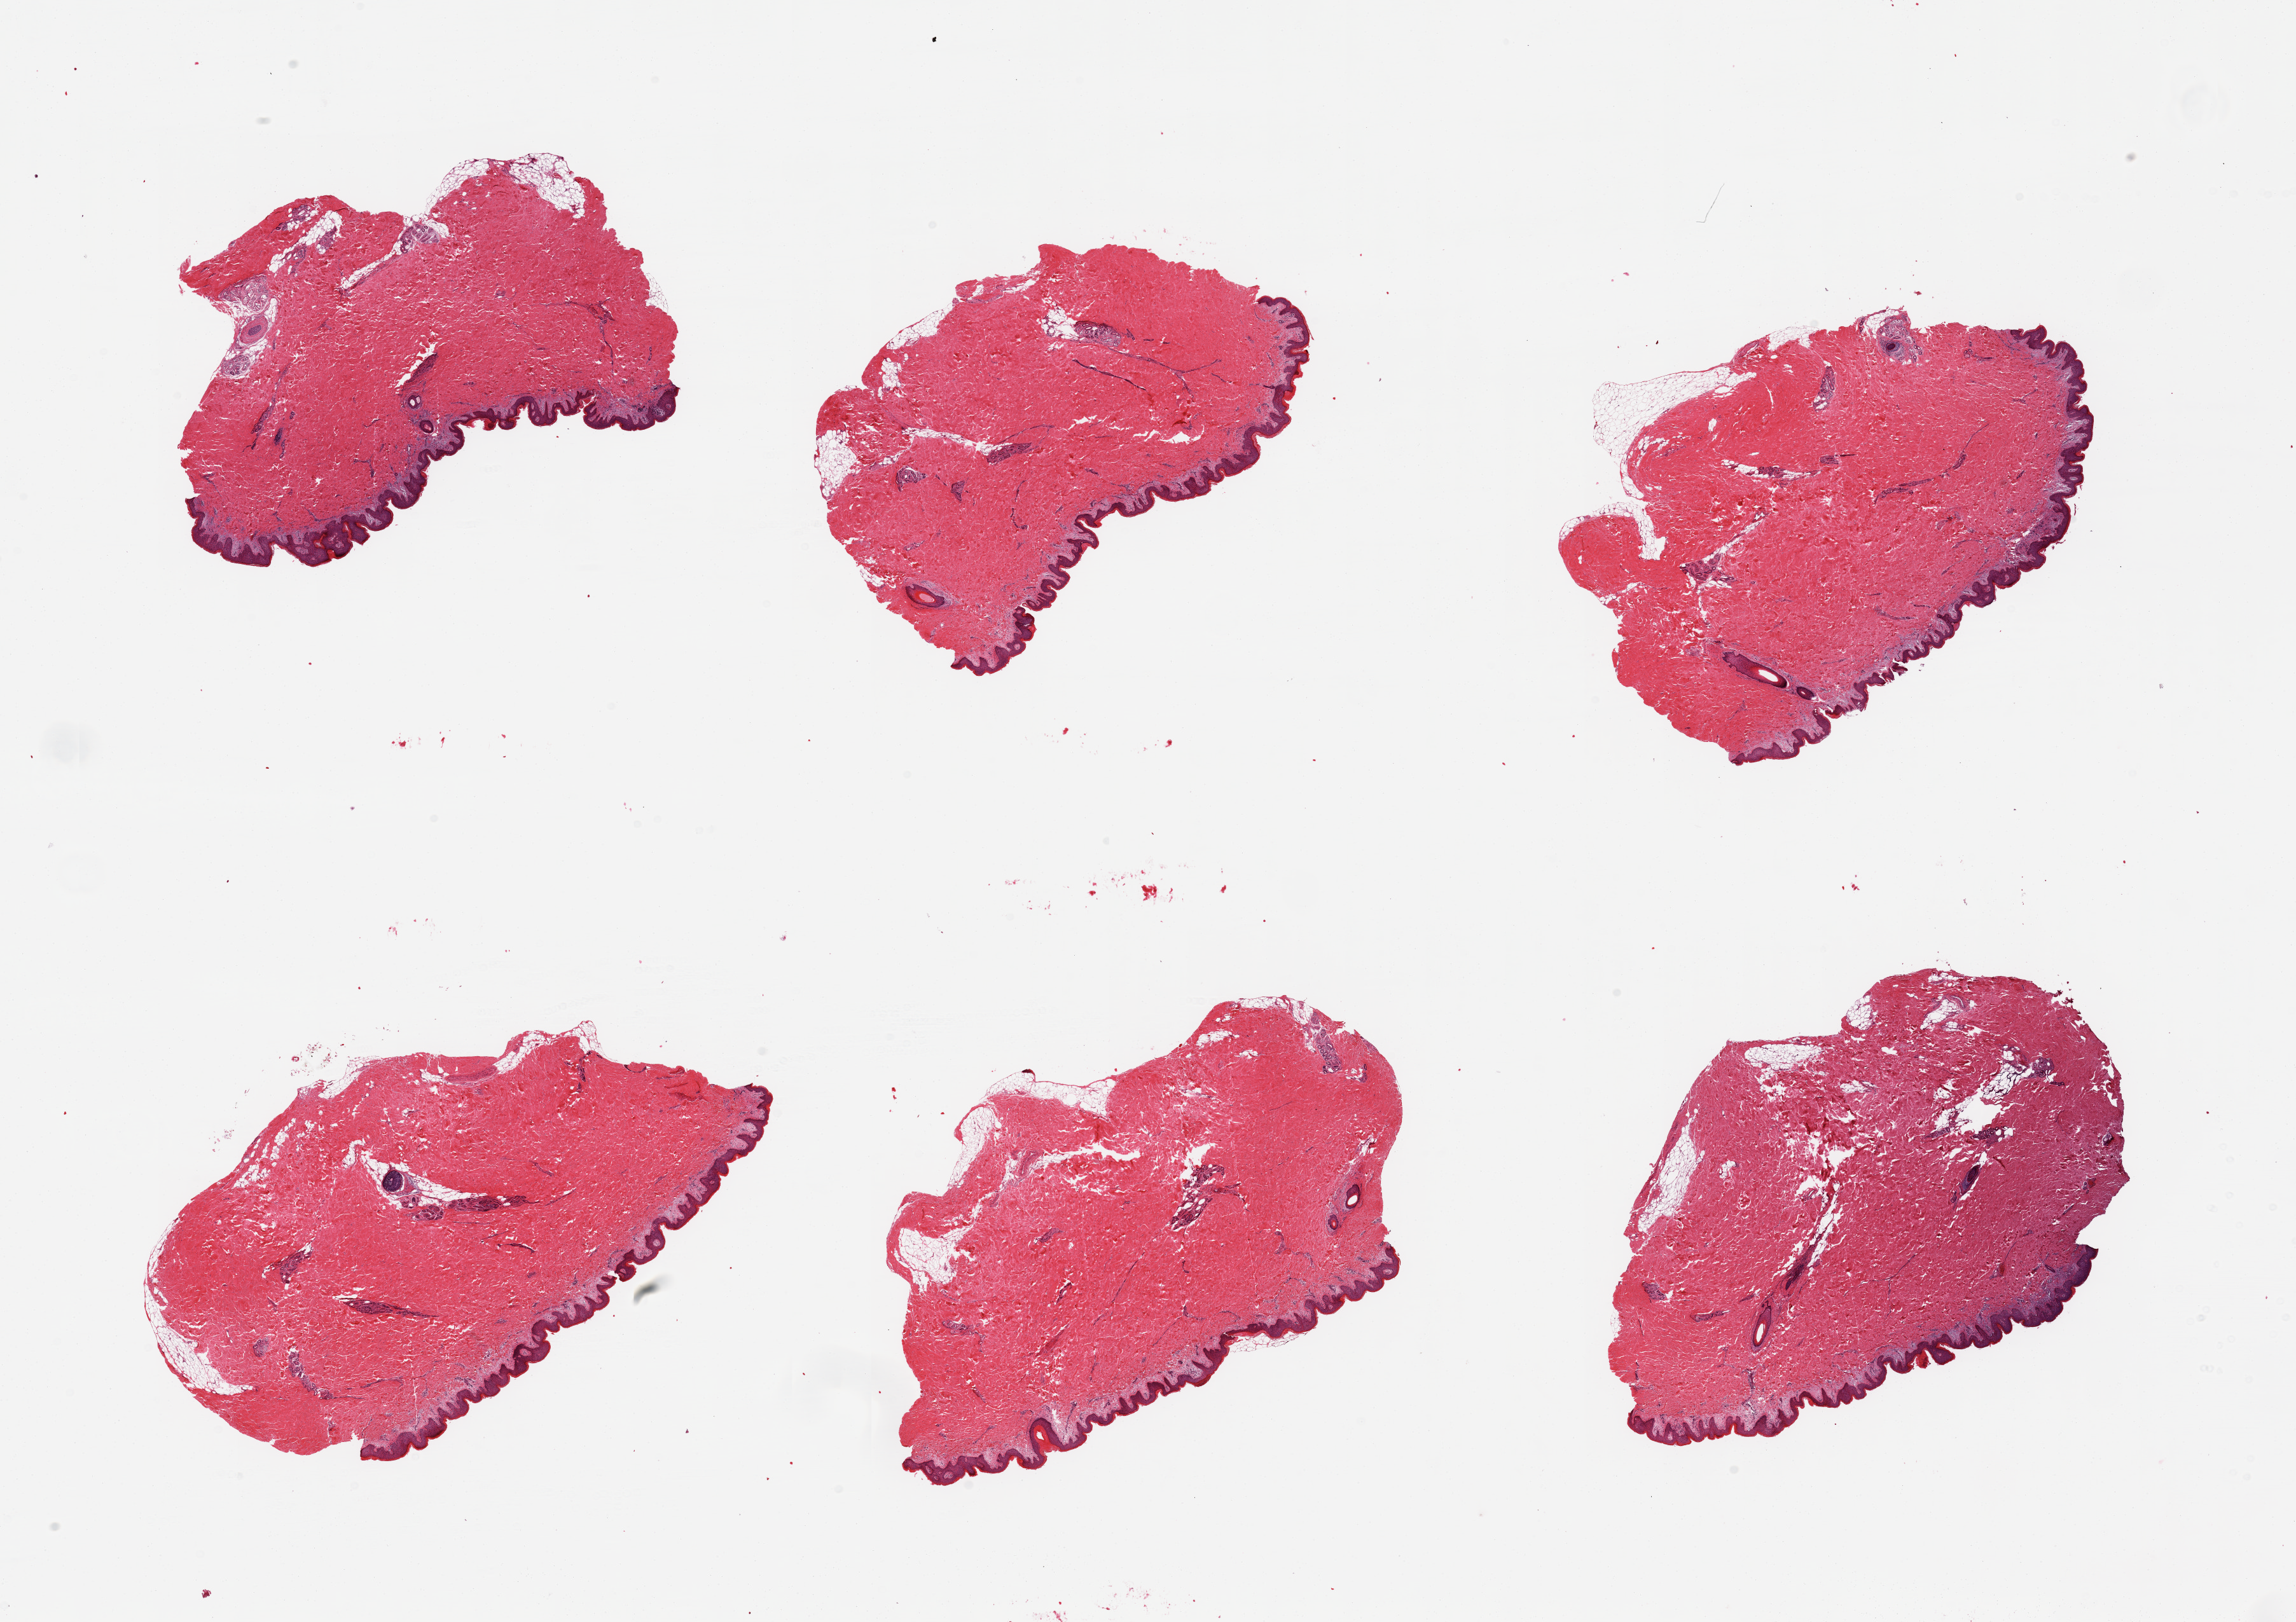
H&E whole-slide image, a low-resolution overview of the entire scanned area, about 28.5 x 20.2 mm (acquisition: 20x scan). PAXgene-fixed, paraffin-embedded tissue. Section of skin of suprapubic region (target tissue). Tissue donor sample. Donor sex: male.
• review note (as recorded): 6 pieces; <10% dermall fat